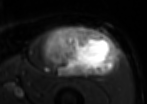
MRI of an extremity soft-tissue mass, one axial slice. Position 52 of 85 along the scan axis. T2-weighted fat-saturated. MR volume resampled by the dataset authors to the PET/CT grid (not the native acquisition matrix). 3.27 mm slice thickness. 147 × 104 image matrix. Male patient. From the clinical record (not read from this slice): histological type: extraskeletal osteosarcoma; grade: high; site of the primary tumour: thigh.
Annotated regions visible in this slice (expert contour drawn on MRI and transferred to this co-registered scan by the dataset authors):
- gross tumour volume (mass): bounding box [x1, y1, x2, y2] px = [42, 26, 118, 77]